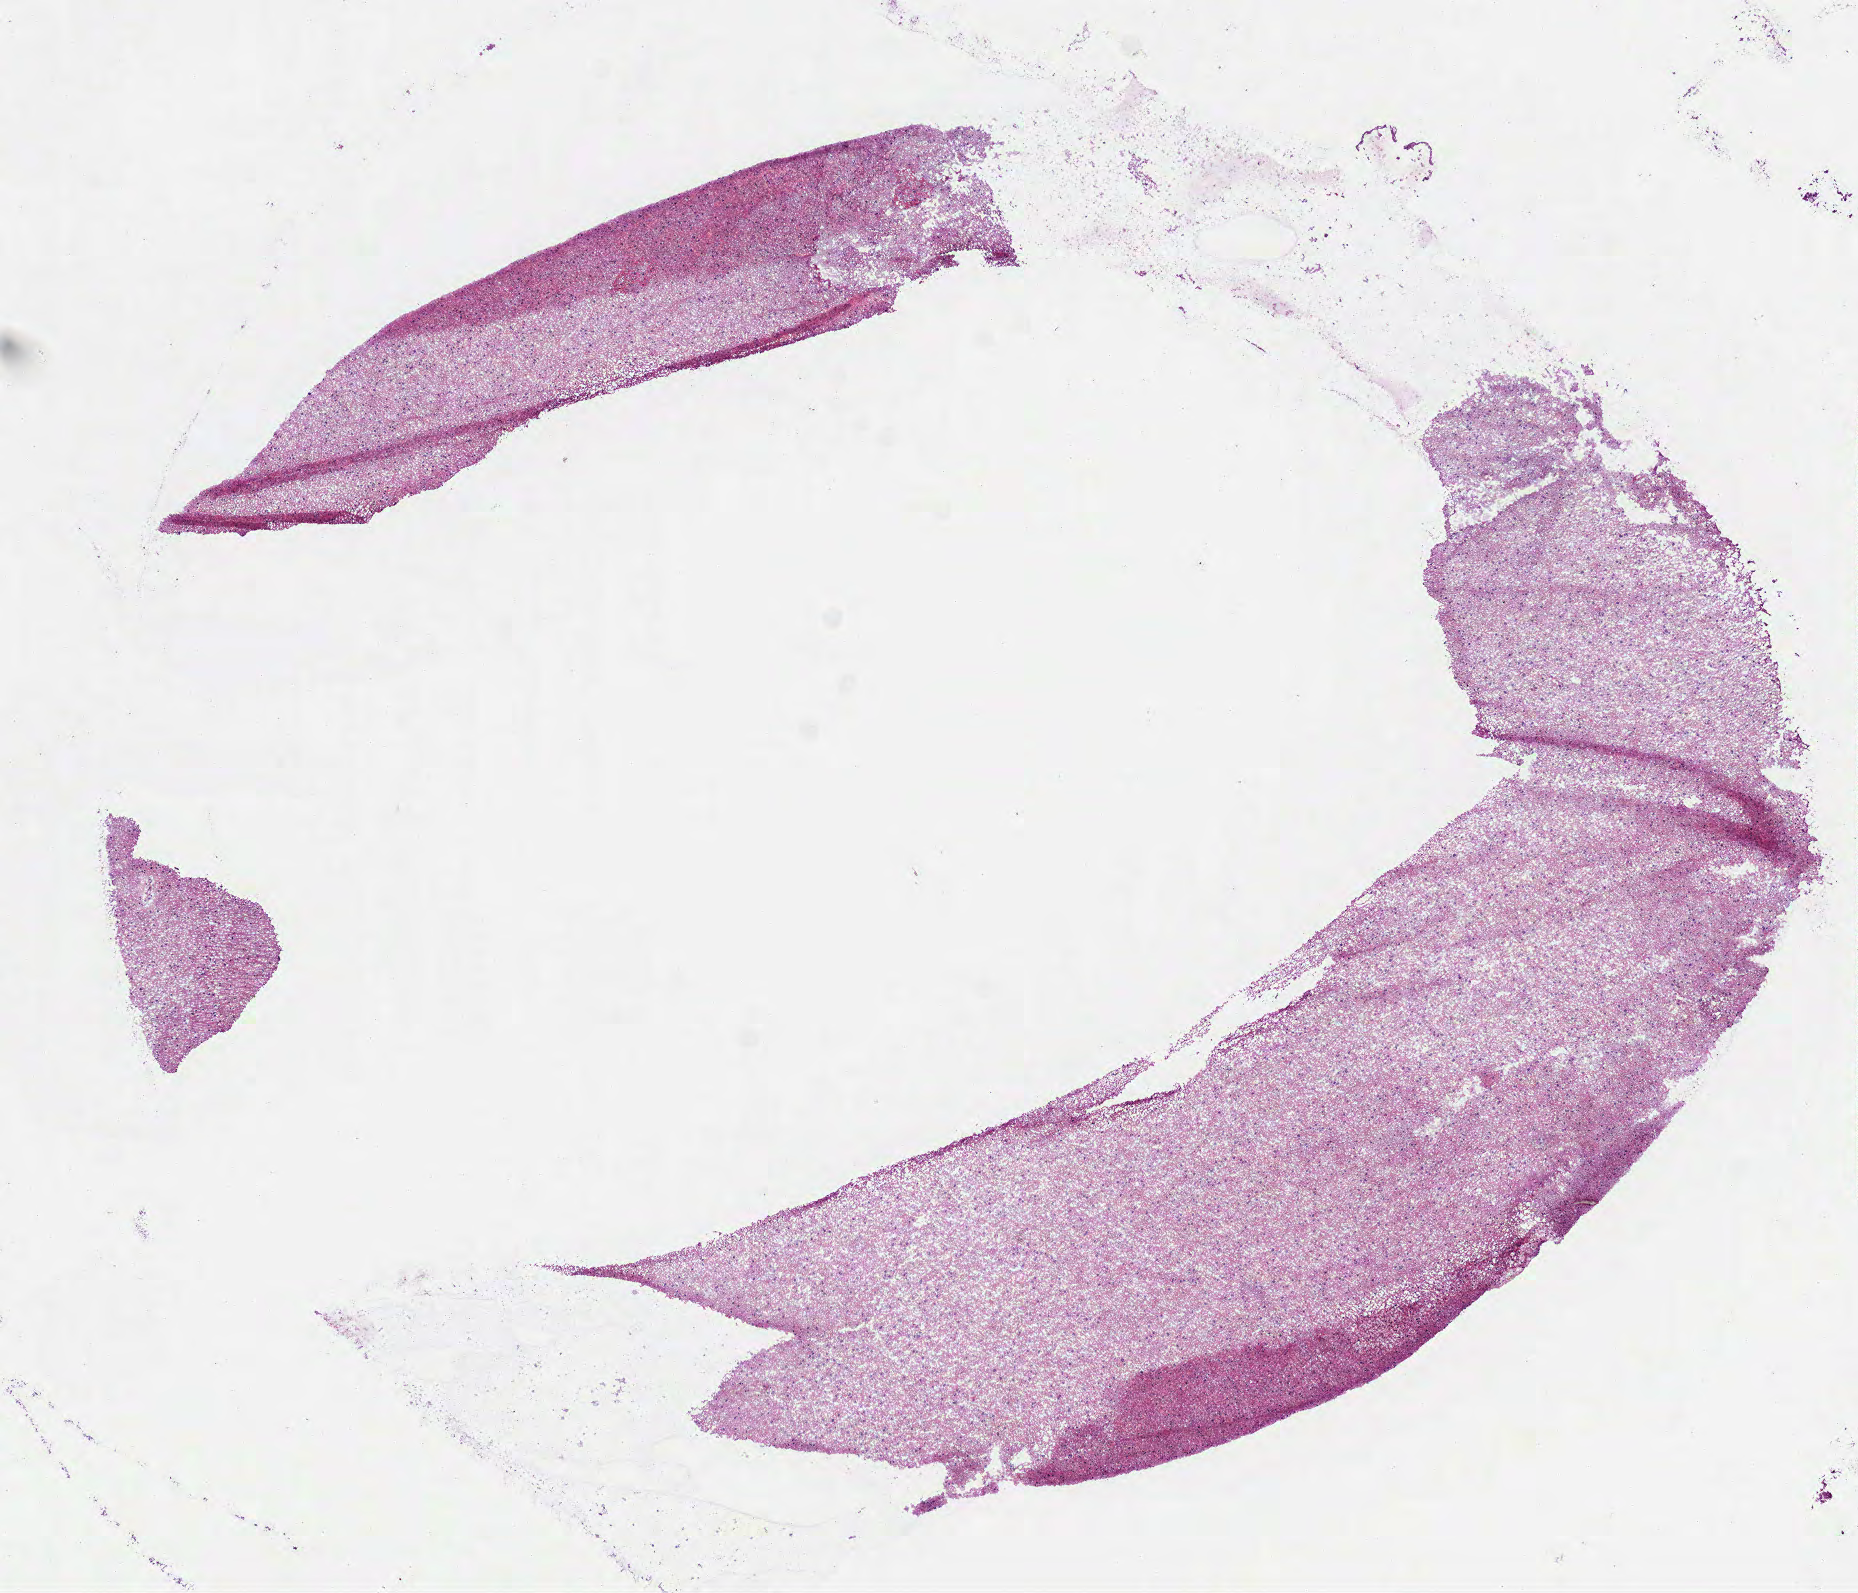
Whole-slide histology image, H&E, low-resolution overview of the scanned area, about 7.5 x 6.4 mm (slide scanned at 40x). Frozen section from the bottom of the tissue portion. Brain, primary tumour sample. Patient: female, age at initial diagnosis 18 years. Slide review estimates, as recorded: tumour cells 100%, tumour nuclei 65%.
Diagnosis: Mixed glioma.